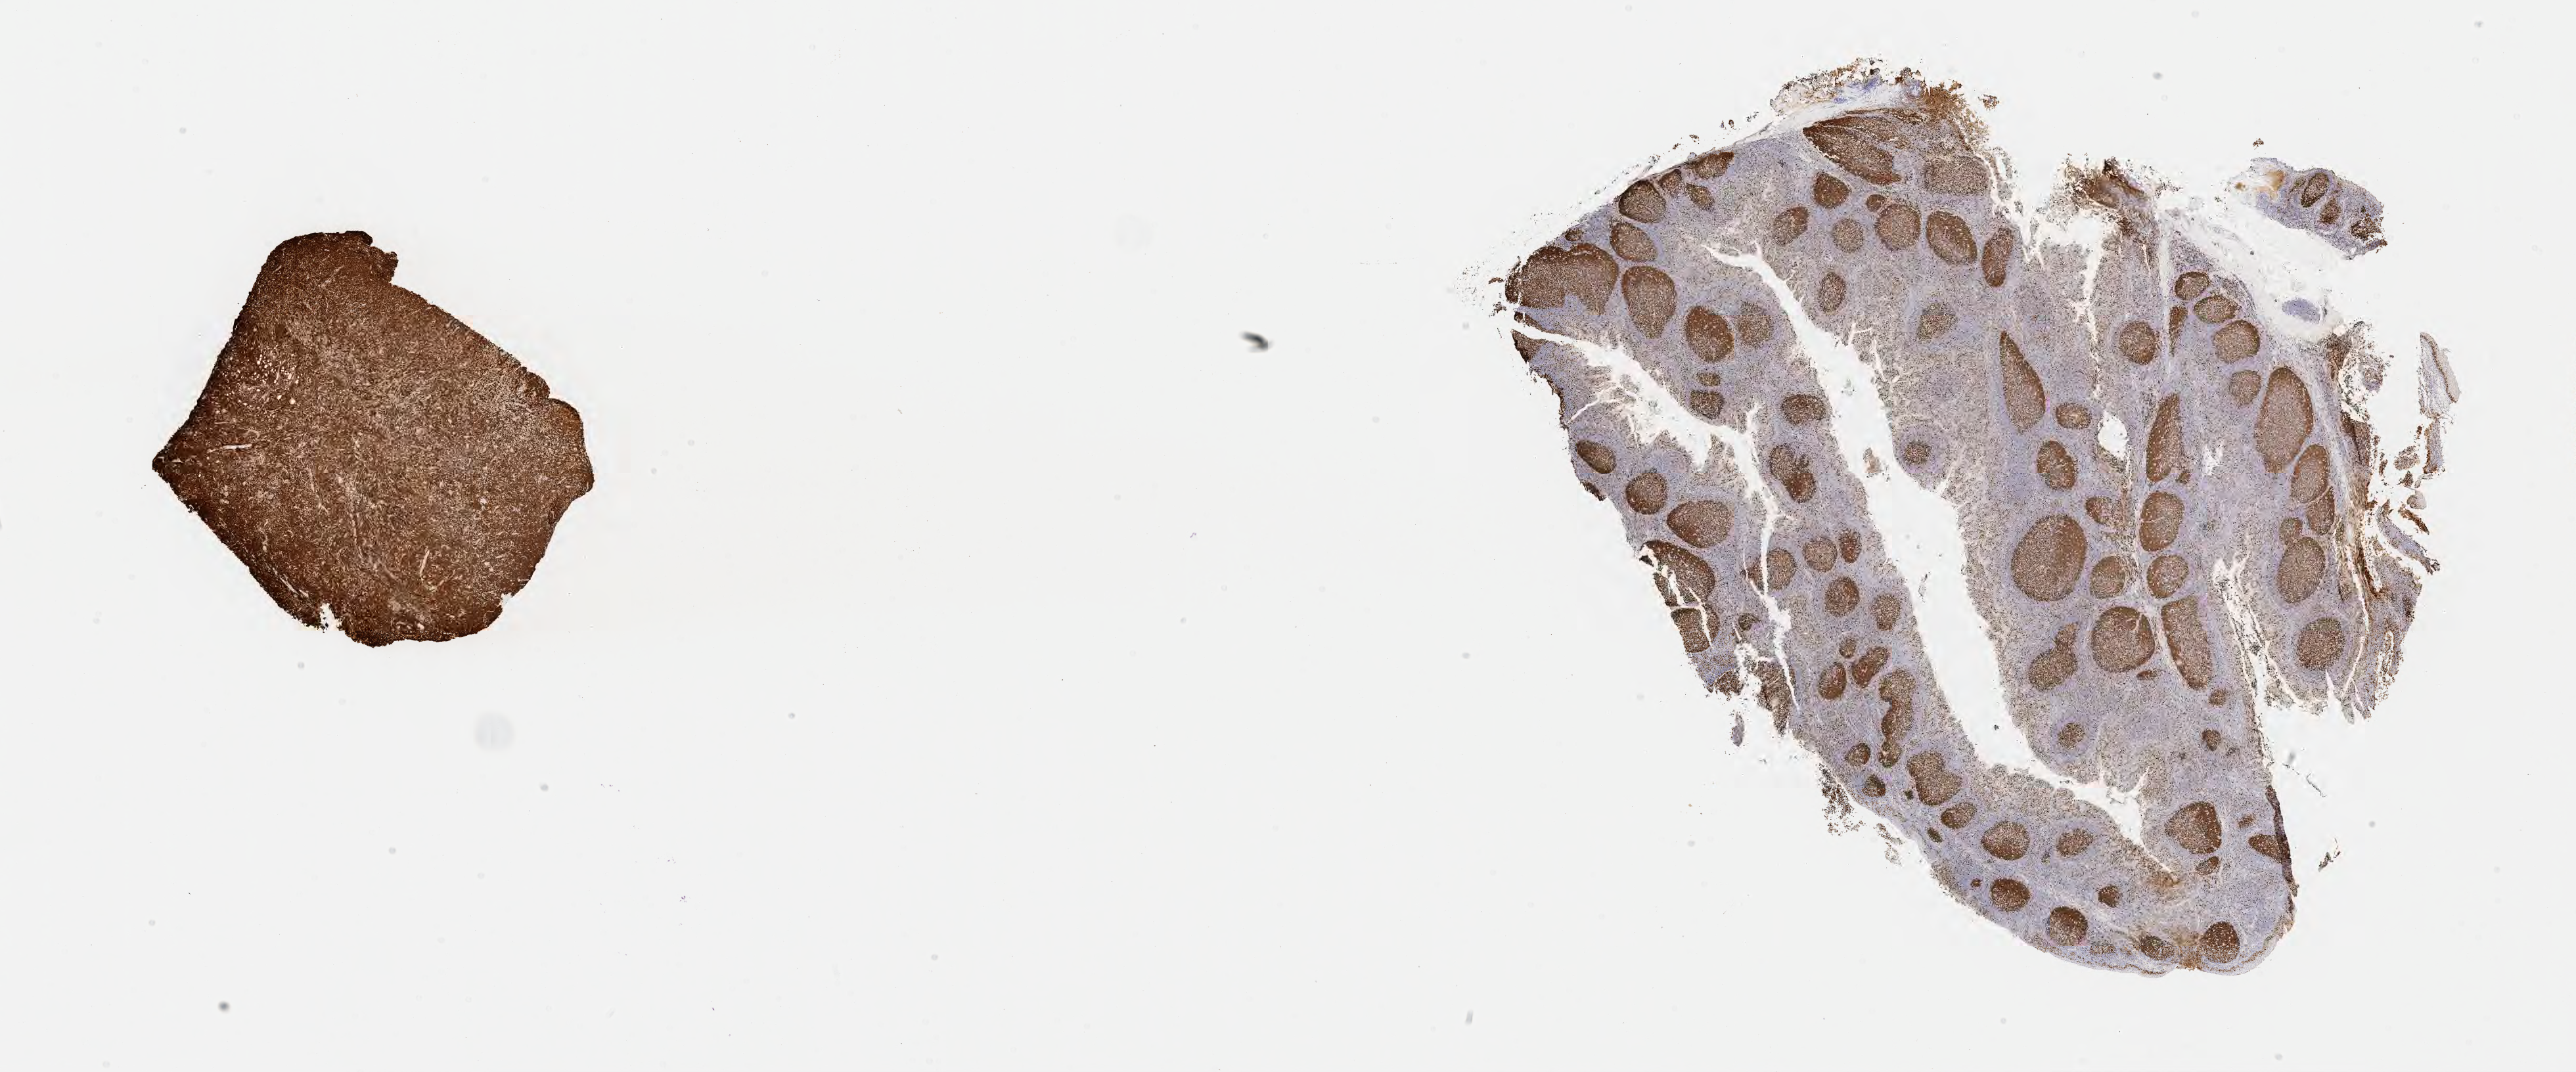
Immunohistochemistry (IHC) whole-slide image stained for Ki-67, a low-resolution overview of the entire scanned area, about 31.7 x 13.2 mm; specimen: tumor tissue; site: buccal mucosa. Male patient; age at initial diagnosis 7 years.
- diagnosis: Burkitt lymphoma, NOS